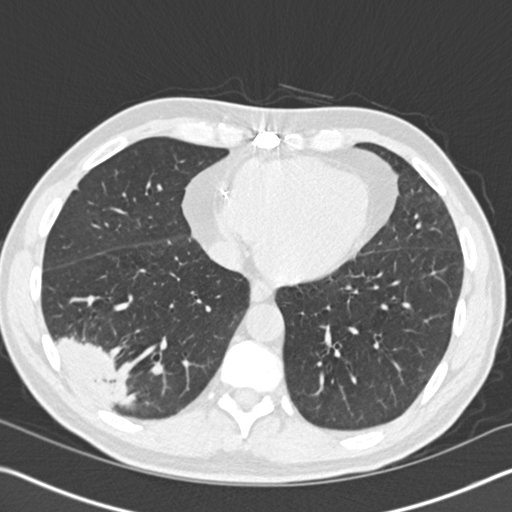
Axial slice from a low-dose chest CT screening exam; baseline annual screen; lung window (W 1500 / L -600 HU); 120 kVp. Male participant, aged 61 years at enrolment. Current smoker at enrolment.
Lesion marked by an expert reader, bounding box [x1, y1, x2, y2] px = [31, 303, 148, 419]. Screening reader's record for this exam (one nodule recorded; not confirmed to be the boxed lesion): non-calcified nodule or mass ≥4 mm, right lower lobe, 52 × 36 mm, spiculated (stellate) margins, soft tissue attenuation. Official screen result: positive, change unspecified: nodule(s) >= 4 mm or enlarging nodule(s), mass(es), or other non-specific abnormalities suspicious for lung cancer.